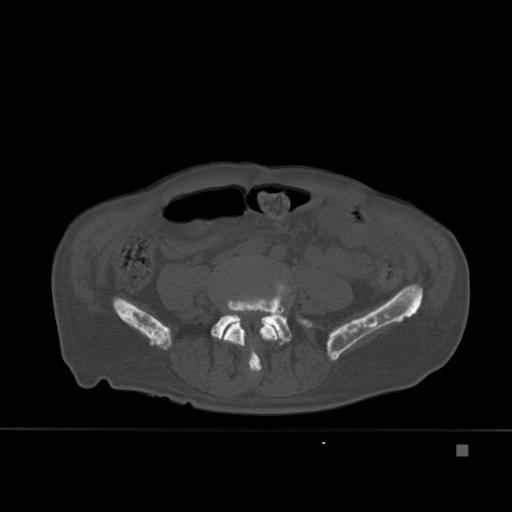
CT including the spine, one axial slice; bone window (W 1800 / L 400 HU); 1.5 mm slice thickness; 512 × 512 image matrix, field of view 378 × 378 mm. Male patient, age 75 years. Case-level facts recorded for this patient, not image findings: primary cancer: prostate.
Annotated regions visible in this slice (semi-automatic segmentation, software-assisted and operator-edited):
- L4 vertebra: bounding box (x1, y1, x2, y2) in pixels: (223, 298, 279, 377)
- L5 vertebra: (211, 281, 312, 368)
- T7 vertebra: (264, 308, 283, 316)